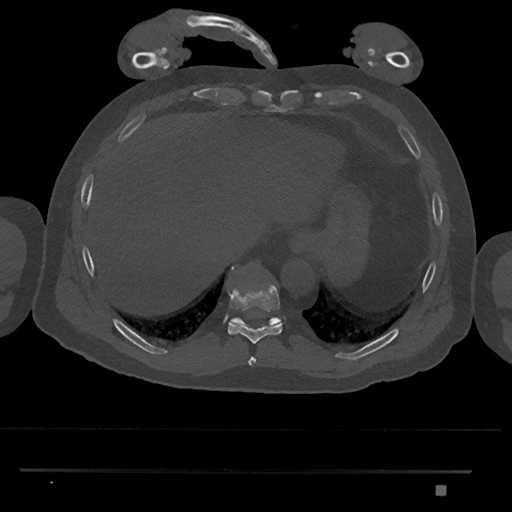
CT including the spine, one axial slice; 120 kVp; bone window (W 1800 / L 400 HU); 0.5 mm slice thickness; 512 × 512 image matrix, field of view 429 × 429 mm. Patient: male, 65 years. Case-level facts recorded for this patient, not image findings: primary cancer: prostate.
Structures marked on this image (semi-automatic segmentation, software-assisted and operator-edited):
- T10 vertebra: bounding box [x1, y1, x2, y2] px = [231, 317, 282, 326]
- T8 vertebra: [248, 357, 256, 366]
- T9 vertebra: [228, 285, 282, 344]